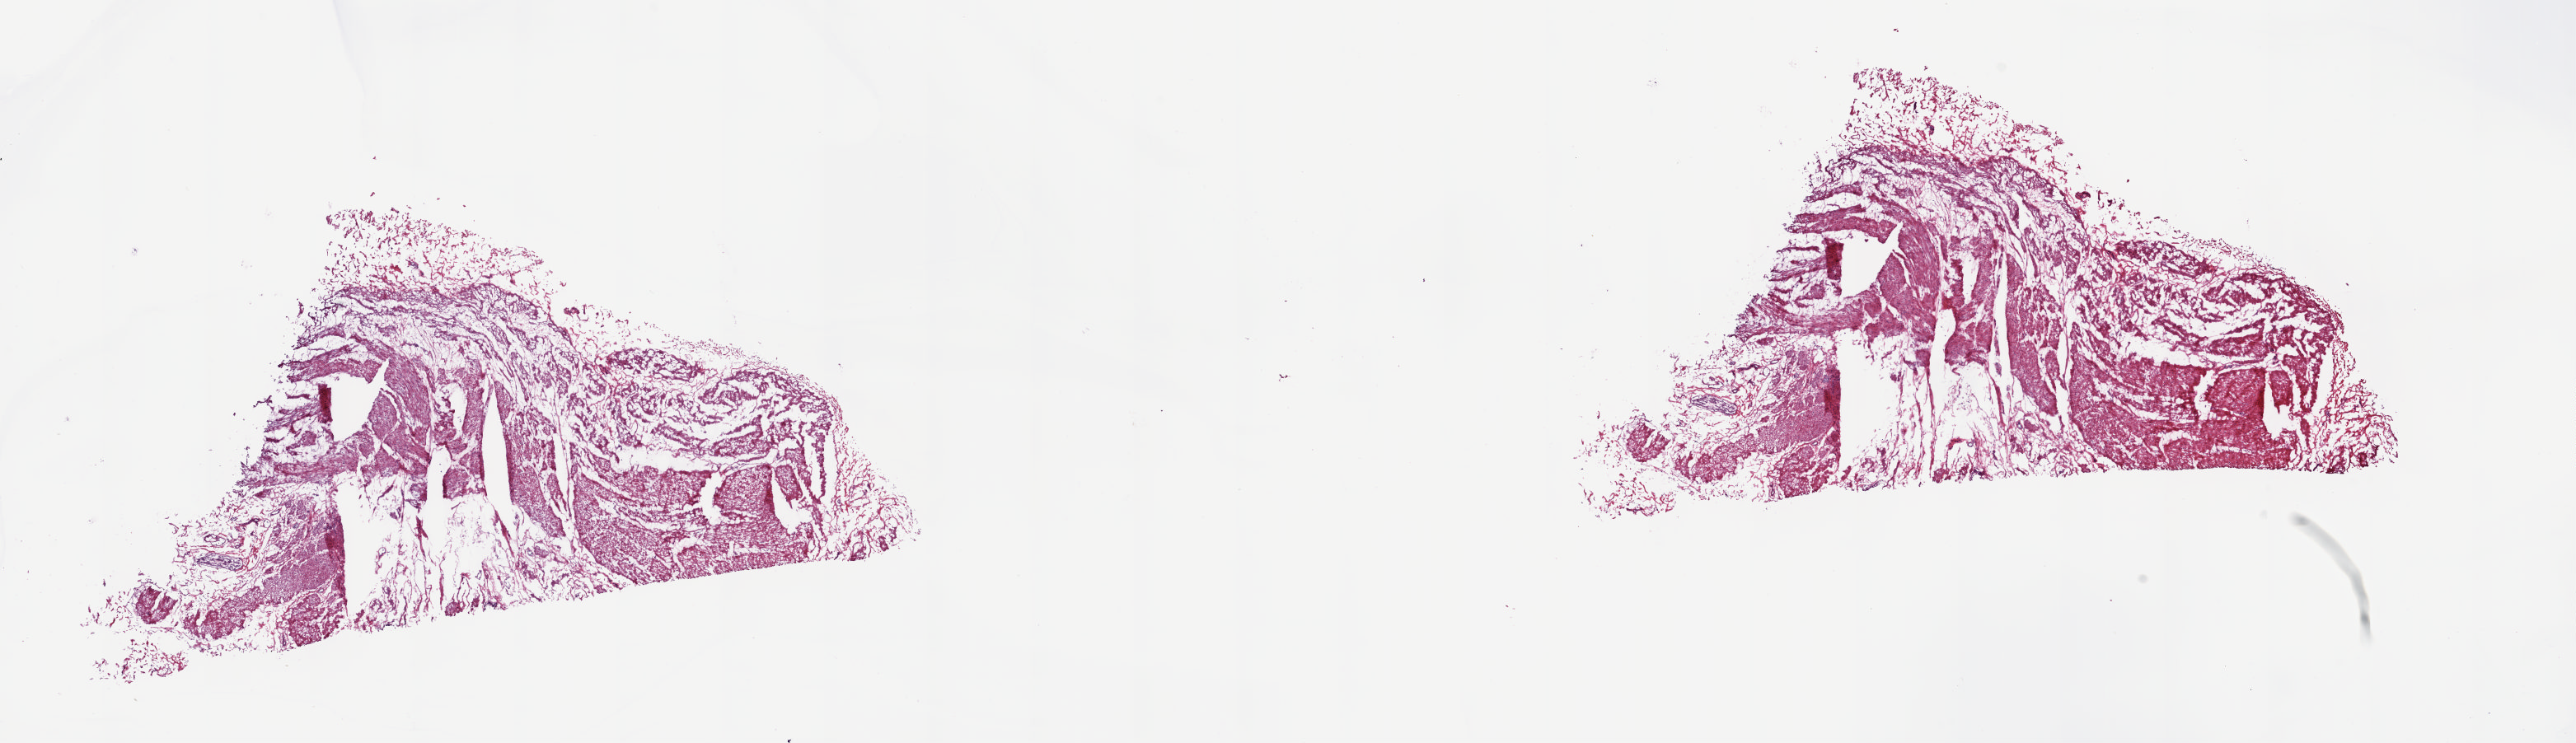
Whole-slide histology image, H&E, low-resolution overview of the scanned area, about 24.8 x 7.2 mm. Frozen section. Sample: solid tissue normal (non-tumour tissue), esophagus. Male, age 68 years at initial diagnosis. Slide review estimates, as recorded: tumour cells 0%, tumour nuclei 0%, normal cells 20%, stromal cells 80%, necrosis 0%. Infiltration values recorded for this section: lymphocyte infiltration 40%, monocyte infiltration 20%, neutrophil infiltration 20%.
This section: solid tissue normal (non-tumour) sample from the same patient. Patient diagnosis: Adenocarcinoma, NOS.